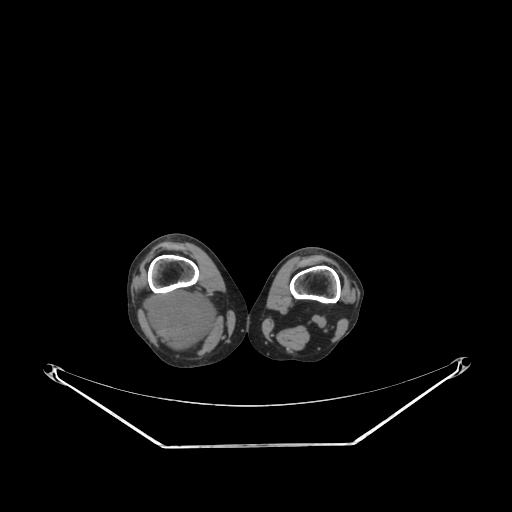
CT of an extremity soft-tissue mass (from a PET/CT study), one axial slice. Slice 180 of 267 in the series (ordered by position). Reconstruction kernel SOFT. 140 kVp. Soft-tissue window (W 400 / L 40 HU). 512 × 512 image matrix, field of view 500 × 500 mm. Female patient. Case-level facts recorded for this patient, not image findings: histological type: liposarcoma; site of the primary tumour: right thigh.
Structures marked on this image (expert contour drawn on MRI and transferred to this co-registered scan by the dataset authors):
- gross tumour volume (mass): bounding box (x1, y1, x2, y2) in pixels: (144, 290, 218, 353)